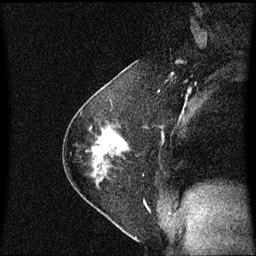
Breast MRI (dynamic contrast-enhanced), one sagittal slice. Position 37 of 60 along the scan axis. Dynamic contrast-enhanced series, image 2 of 3 at this slice position (ordered by acquisition). 1.5 T. TE 4.2 ms, TR 8.4 ms. 2 mm slice thickness. 256 × 256 image matrix. Patient: female, 54 years. Case-level facts recorded for this patient, not image findings: setting: breast cancer imaged before/during neoadjuvant chemotherapy; receptor status: HER2-positive.
Annotated regions visible in this slice (semi-automatically segmented with operator editing):
- analysis volume of interest (the breast-tissue region the enhancement analysis was run in; not a lesion): bounding box (x1, y1, x2, y2) in pixels: (77, 126, 129, 190)
- tumour enhancement mask (voxels above the 70 % enhancement threshold inside the analysis volume of interest): (104, 131, 128, 151)